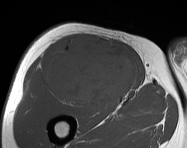
MRI of an extremity soft-tissue mass, one axial slice; MR volume resampled by the dataset authors to the PET/CT grid (not the native acquisition matrix); 187 × 148 image matrix, field of view 183 × 145 mm. Male patient. From the clinical record (not read from this slice): histological type: pleiomorphic leiomyosarcoma; grade: intermediate; site of the primary tumour: right thigh.
Structures marked on this image (expert contour drawn on MRI and transferred to this co-registered scan by the dataset authors):
- gross tumour volume including surrounding oedema: bounding box <45,35,135,108> (left, top, right, bottom; pixels)
- gross tumour volume (mass): <47,36,135,108>